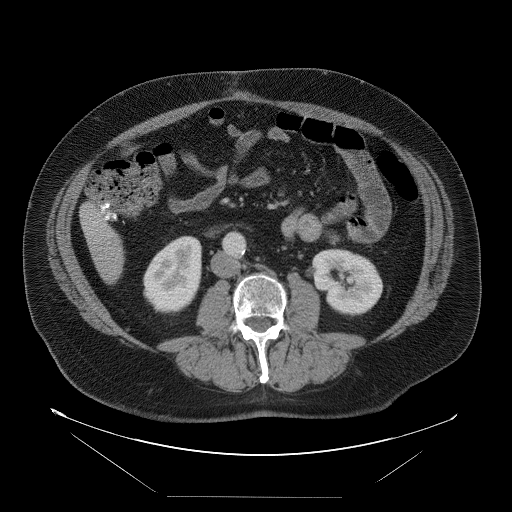
Contrast-enhanced abdominal CT, one axial slice; 120 kVp; intravenous contrast given; soft-tissue window (W 400 / L 40 HU); 5 mm slice thickness; 512 × 512 image matrix. Male patient, age 61 years. Case-level facts recorded for this patient, not image findings: diagnosis: colorectal cancer liver metastases, imaged before liver resection; multiple liver metastases: no; largest metastasis: 6.5 cm.
Annotated regions visible in this slice (outlined manually by an expert reader):
- liver: box from (x=81, y=205) to (x=125, y=283) px